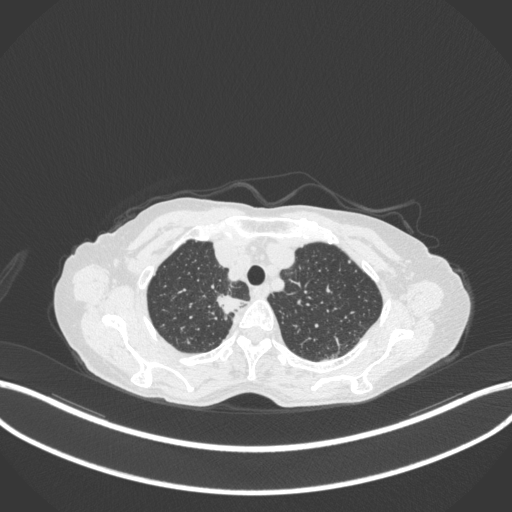
Chest CT, one axial slice. Slice 312 of 363 in the series (ordered by position). Reconstruction kernel B31f. Lung window (W 1500 / L -600 HU). 1 mm slice thickness. 512 × 512 image matrix. Female patient, age 75 years. Case-level facts recorded for this patient, not image findings: clinical TNM (as recorded): T1c N1 M1.
Annotated regions visible in this slice (bounding box drawn by a radiologist):
- lung tumour (recorded histology: adenocarcinoma): bounding box [x1, y1, x2, y2] px = [212, 290, 253, 318]